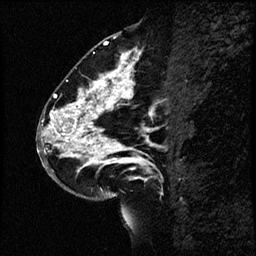
Breast MRI (dynamic contrast-enhanced), one sagittal slice; slice 32 of 60 in the series (ordered by position); dynamic contrast-enhanced study with each time point stored as its own series, time point 2 of 4 at this slice position (early post-contrast, ordered by acquisition time); 1.5 T; TE 4.2 ms, TR 17.6 ms; 2 mm slice thickness; 256 × 256 image matrix. Patient: female, 43 years. Case-level facts recorded for this patient, not image findings: setting: breast cancer imaged before/during neoadjuvant chemotherapy.
Outlined on this slice (semi-automatically segmented with operator editing):
- analysis volume of interest (the breast-tissue region the enhancement analysis was run in; not a lesion): box from (x=39, y=56) to (x=167, y=191) px
- tumour enhancement mask (voxels above the 100 % enhancement threshold inside the analysis volume of interest): (x=41, y=57)–(x=155, y=166)